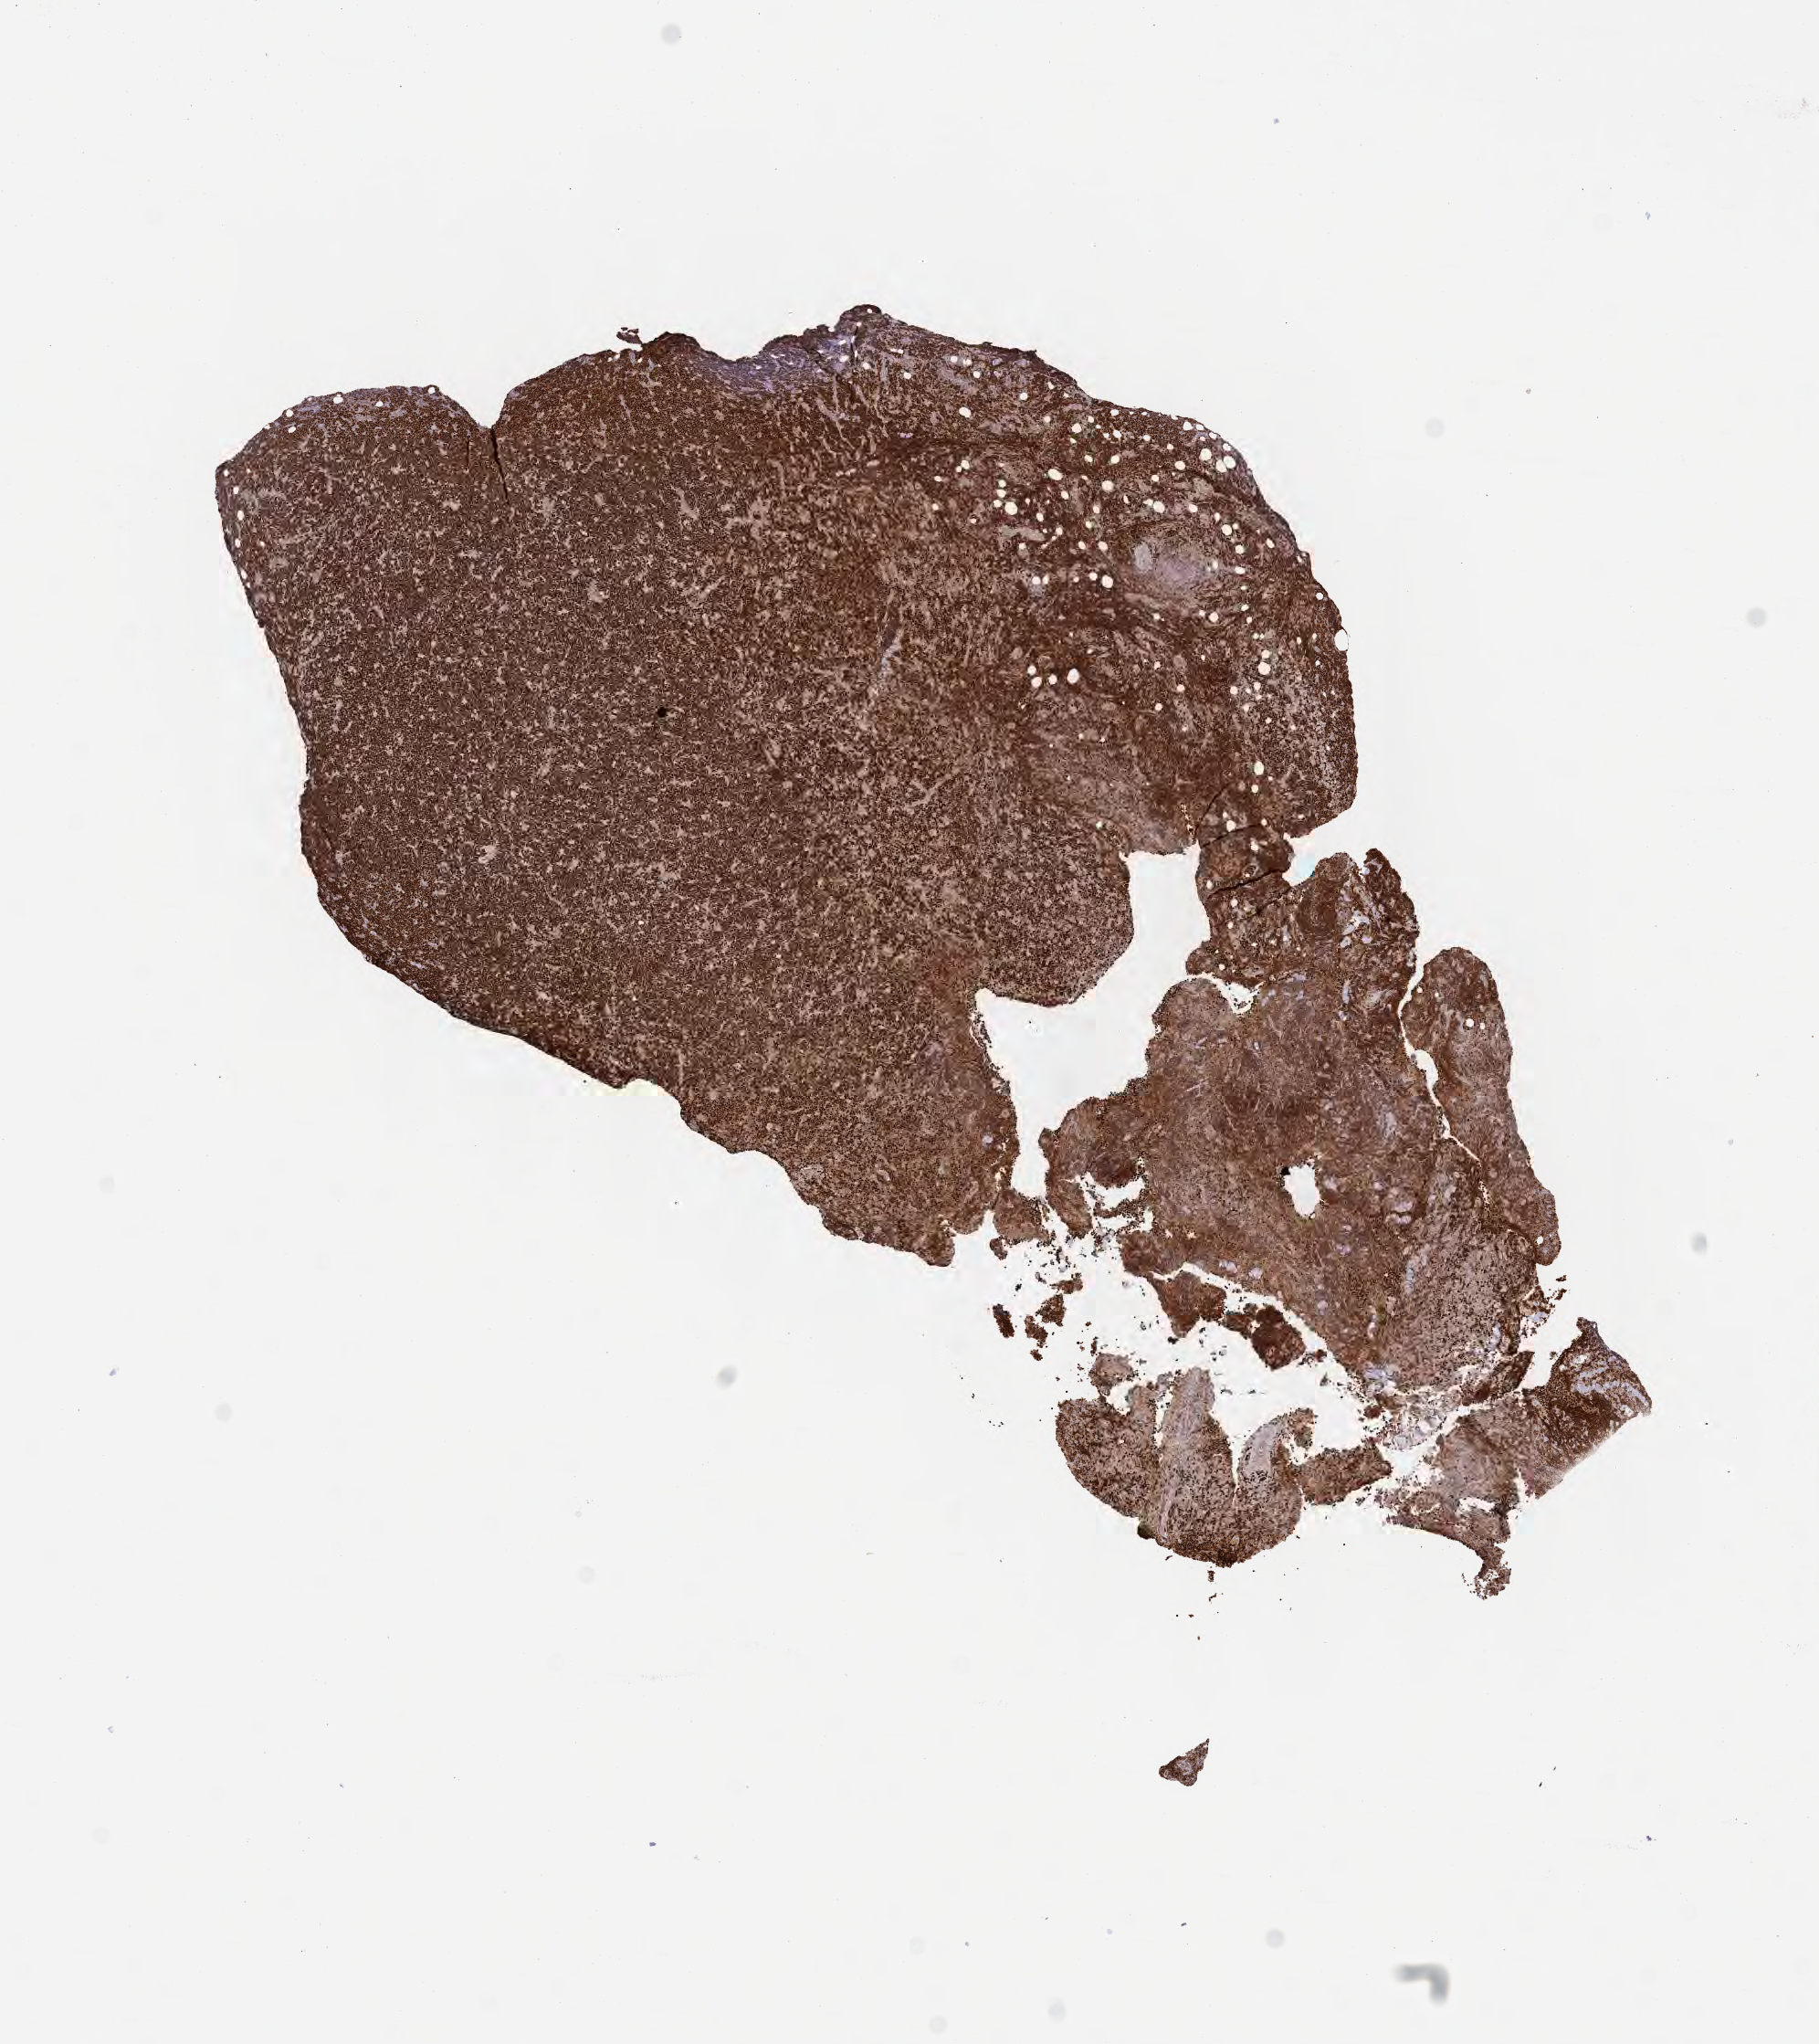
Whole-slide image, immunohistochemical stain for BCL6, a low-resolution overview of the entire scanned area, about 8.0 x 9.0 mm. Tumor tissue. Patient female; 40 years old.
* diagnosis: Burkitt lymphoma, NOS